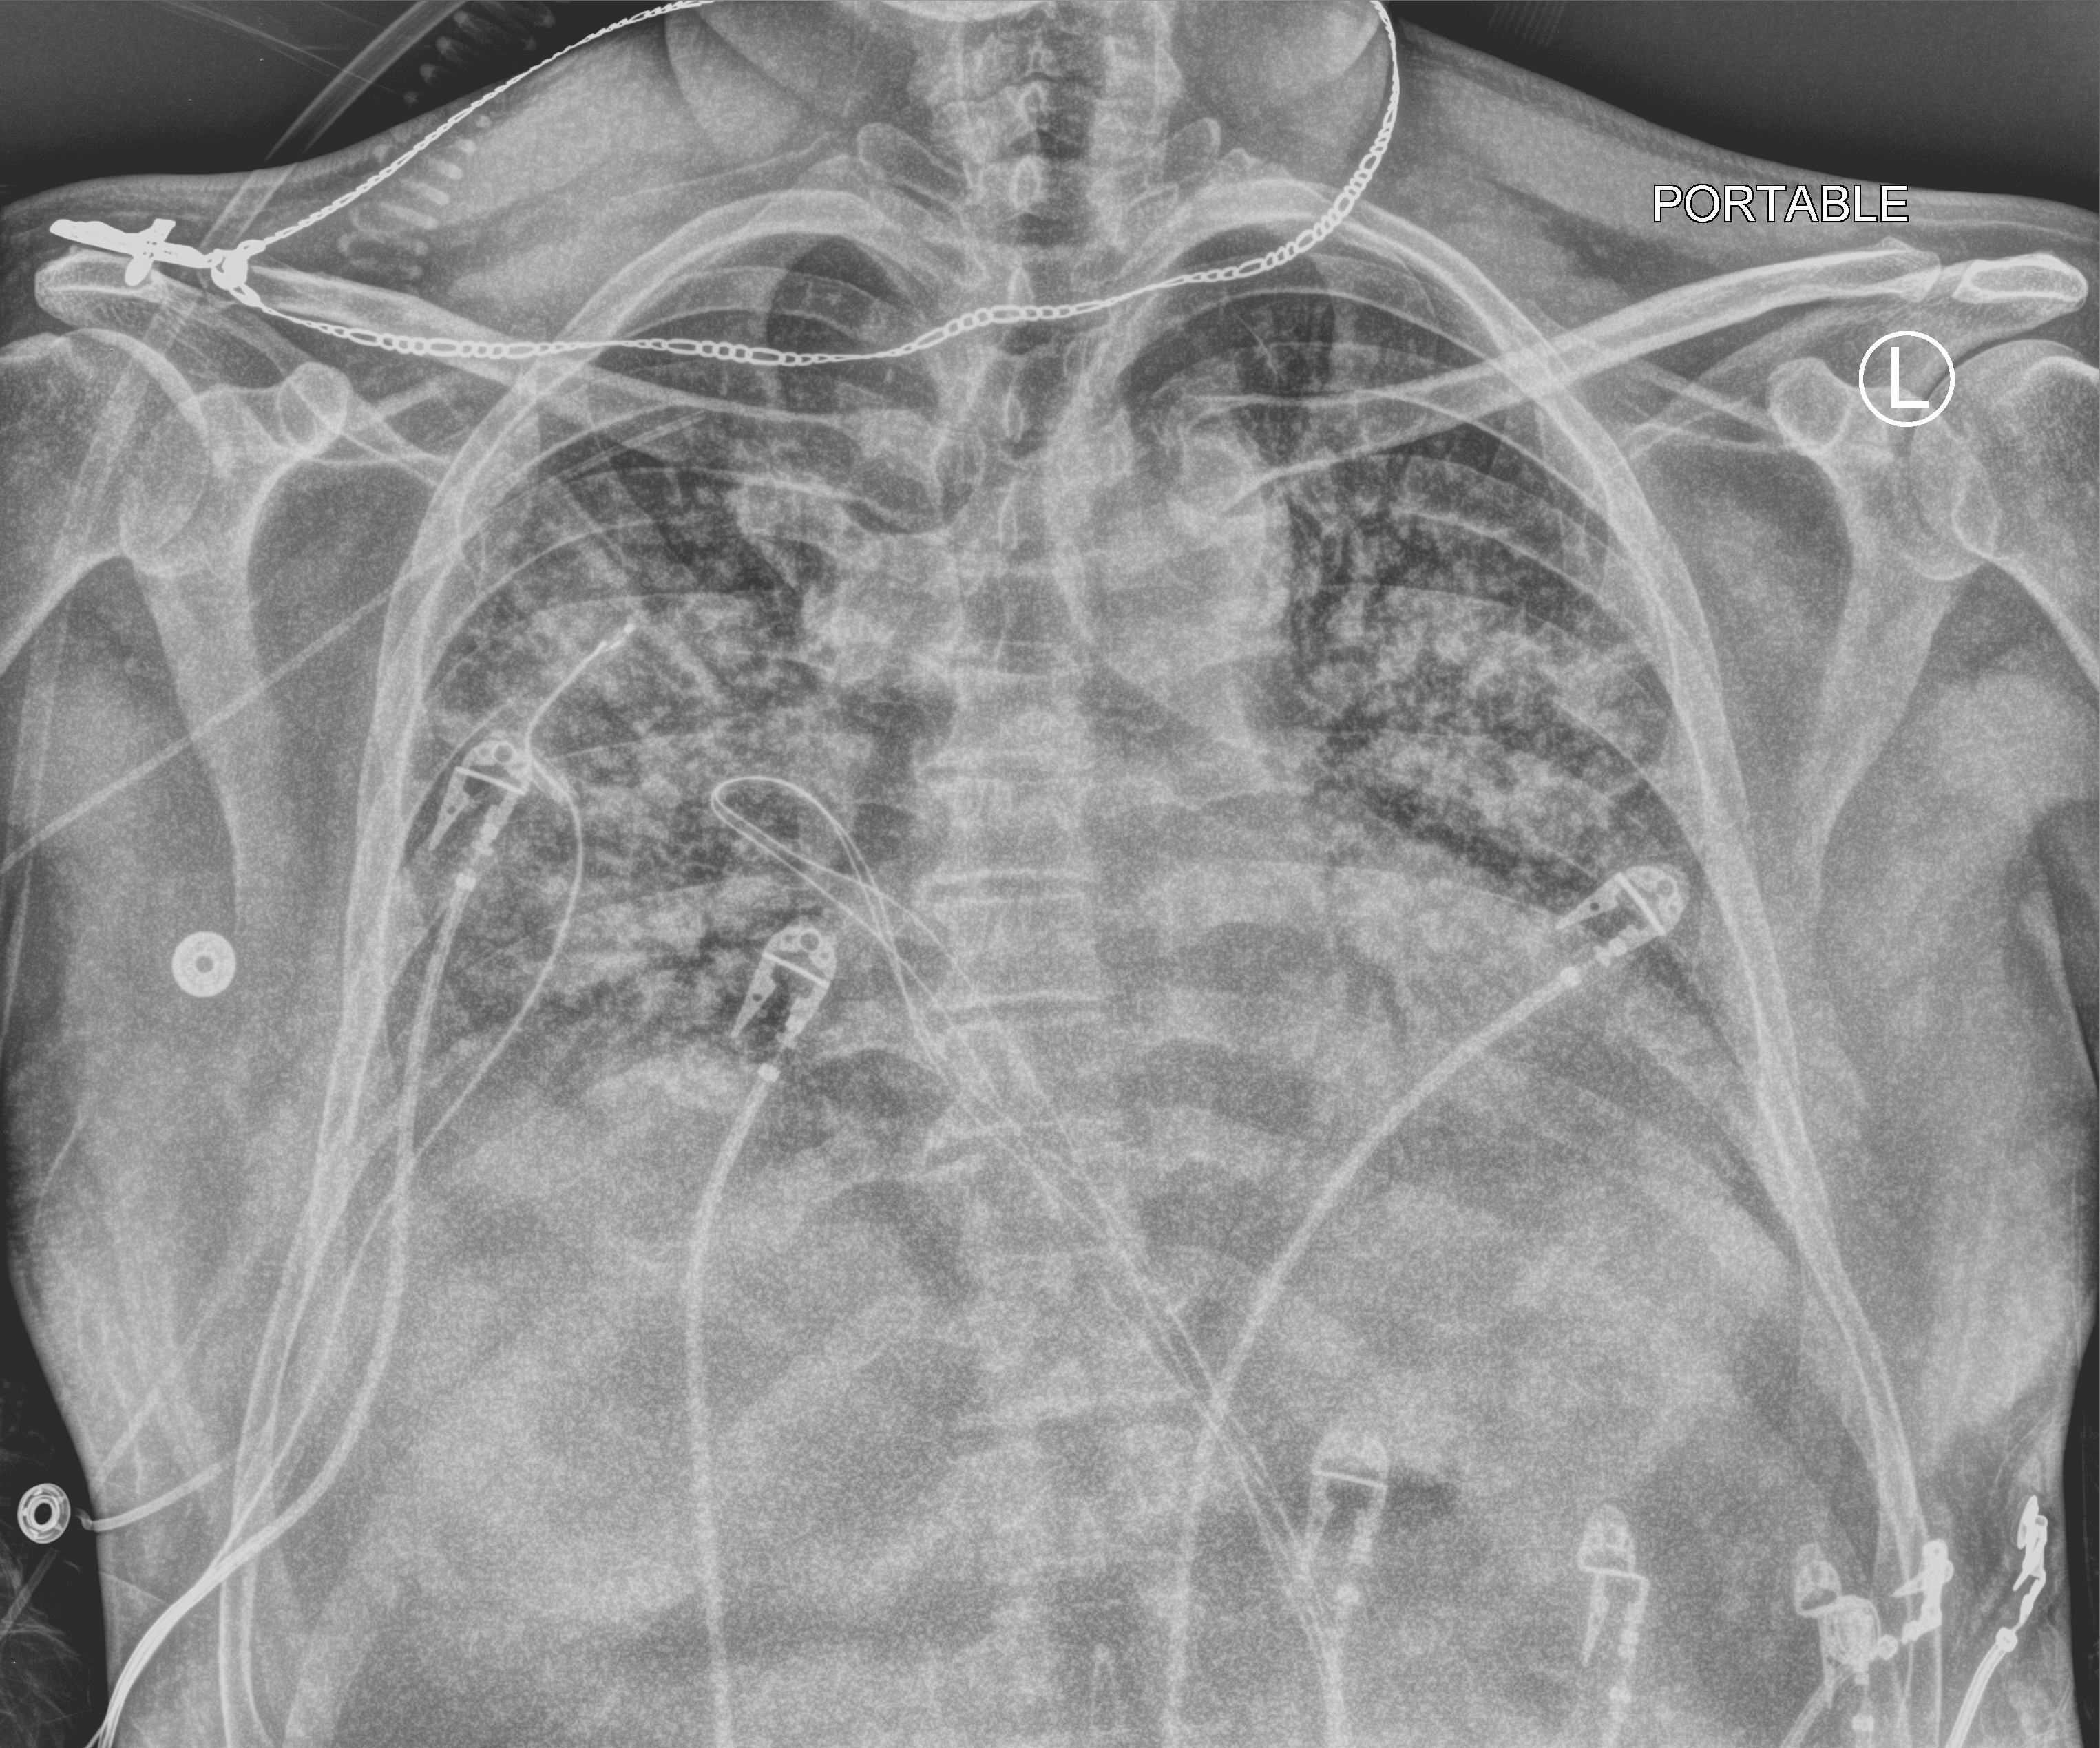
Bedside chest radiograph (computed radiography), anteroposterior (AP) projection. Male patient hospitalised with COVID-19, age 18–59 years.
From the hospital-stay record, not from the radiograph (when in the stay this image was taken is not recorded):
- hypertension (admission record): no
- mechanically ventilated during this hospital stay: yes